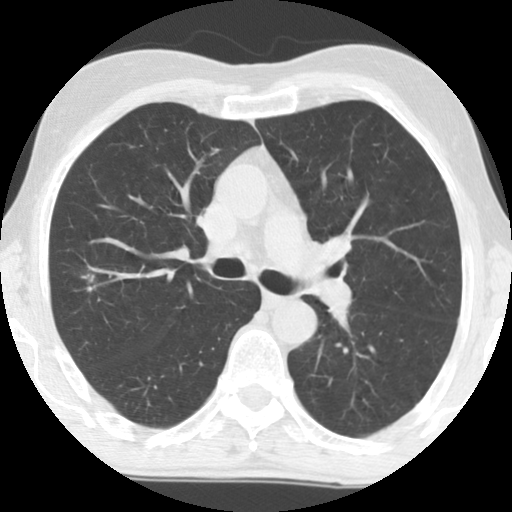
Low-dose screening chest CT, axial slice; first (baseline) screen; lung window (W 1500 / L -600 HU); 2.5 mm slice thickness; 512 × 512 image matrix, field of view 310 × 310 mm. Male, age 69 years at enrolment.
Expert reader's lesion annotation, box from (x=55, y=248) to (x=127, y=316) px. Reader record for this screening exam (exam-level; its link to the box is not recorded): non-calcified nodule or mass ≥4 mm, right upper lobe, 8 × 8 mm, spiculated (stellate) margins, soft tissue attenuation. Official screen result: positive, change unspecified: nodule(s) >= 4 mm or enlarging nodule(s), mass(es), or other non-specific abnormalities suspicious for lung cancer.